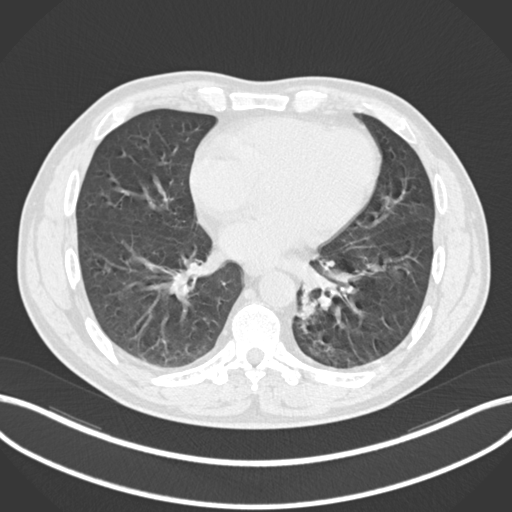
Chest CT, one axial slice; slice 81 of 223 in the series (ordered by position); lung window (W 1500 / L -600 HU); 1 mm slice thickness; 512 × 512 image matrix, field of view 400 × 400 mm. Patient: male, 50 years. Case-level facts recorded for this patient, not image findings: clinical TNM (as recorded): T2a N3 M0.
Structures marked on this image (rectangle marked by the reading radiologist):
- lung tumour (recorded histology: squamous cell carcinoma): box from (x=294, y=292) to (x=318, y=325) px